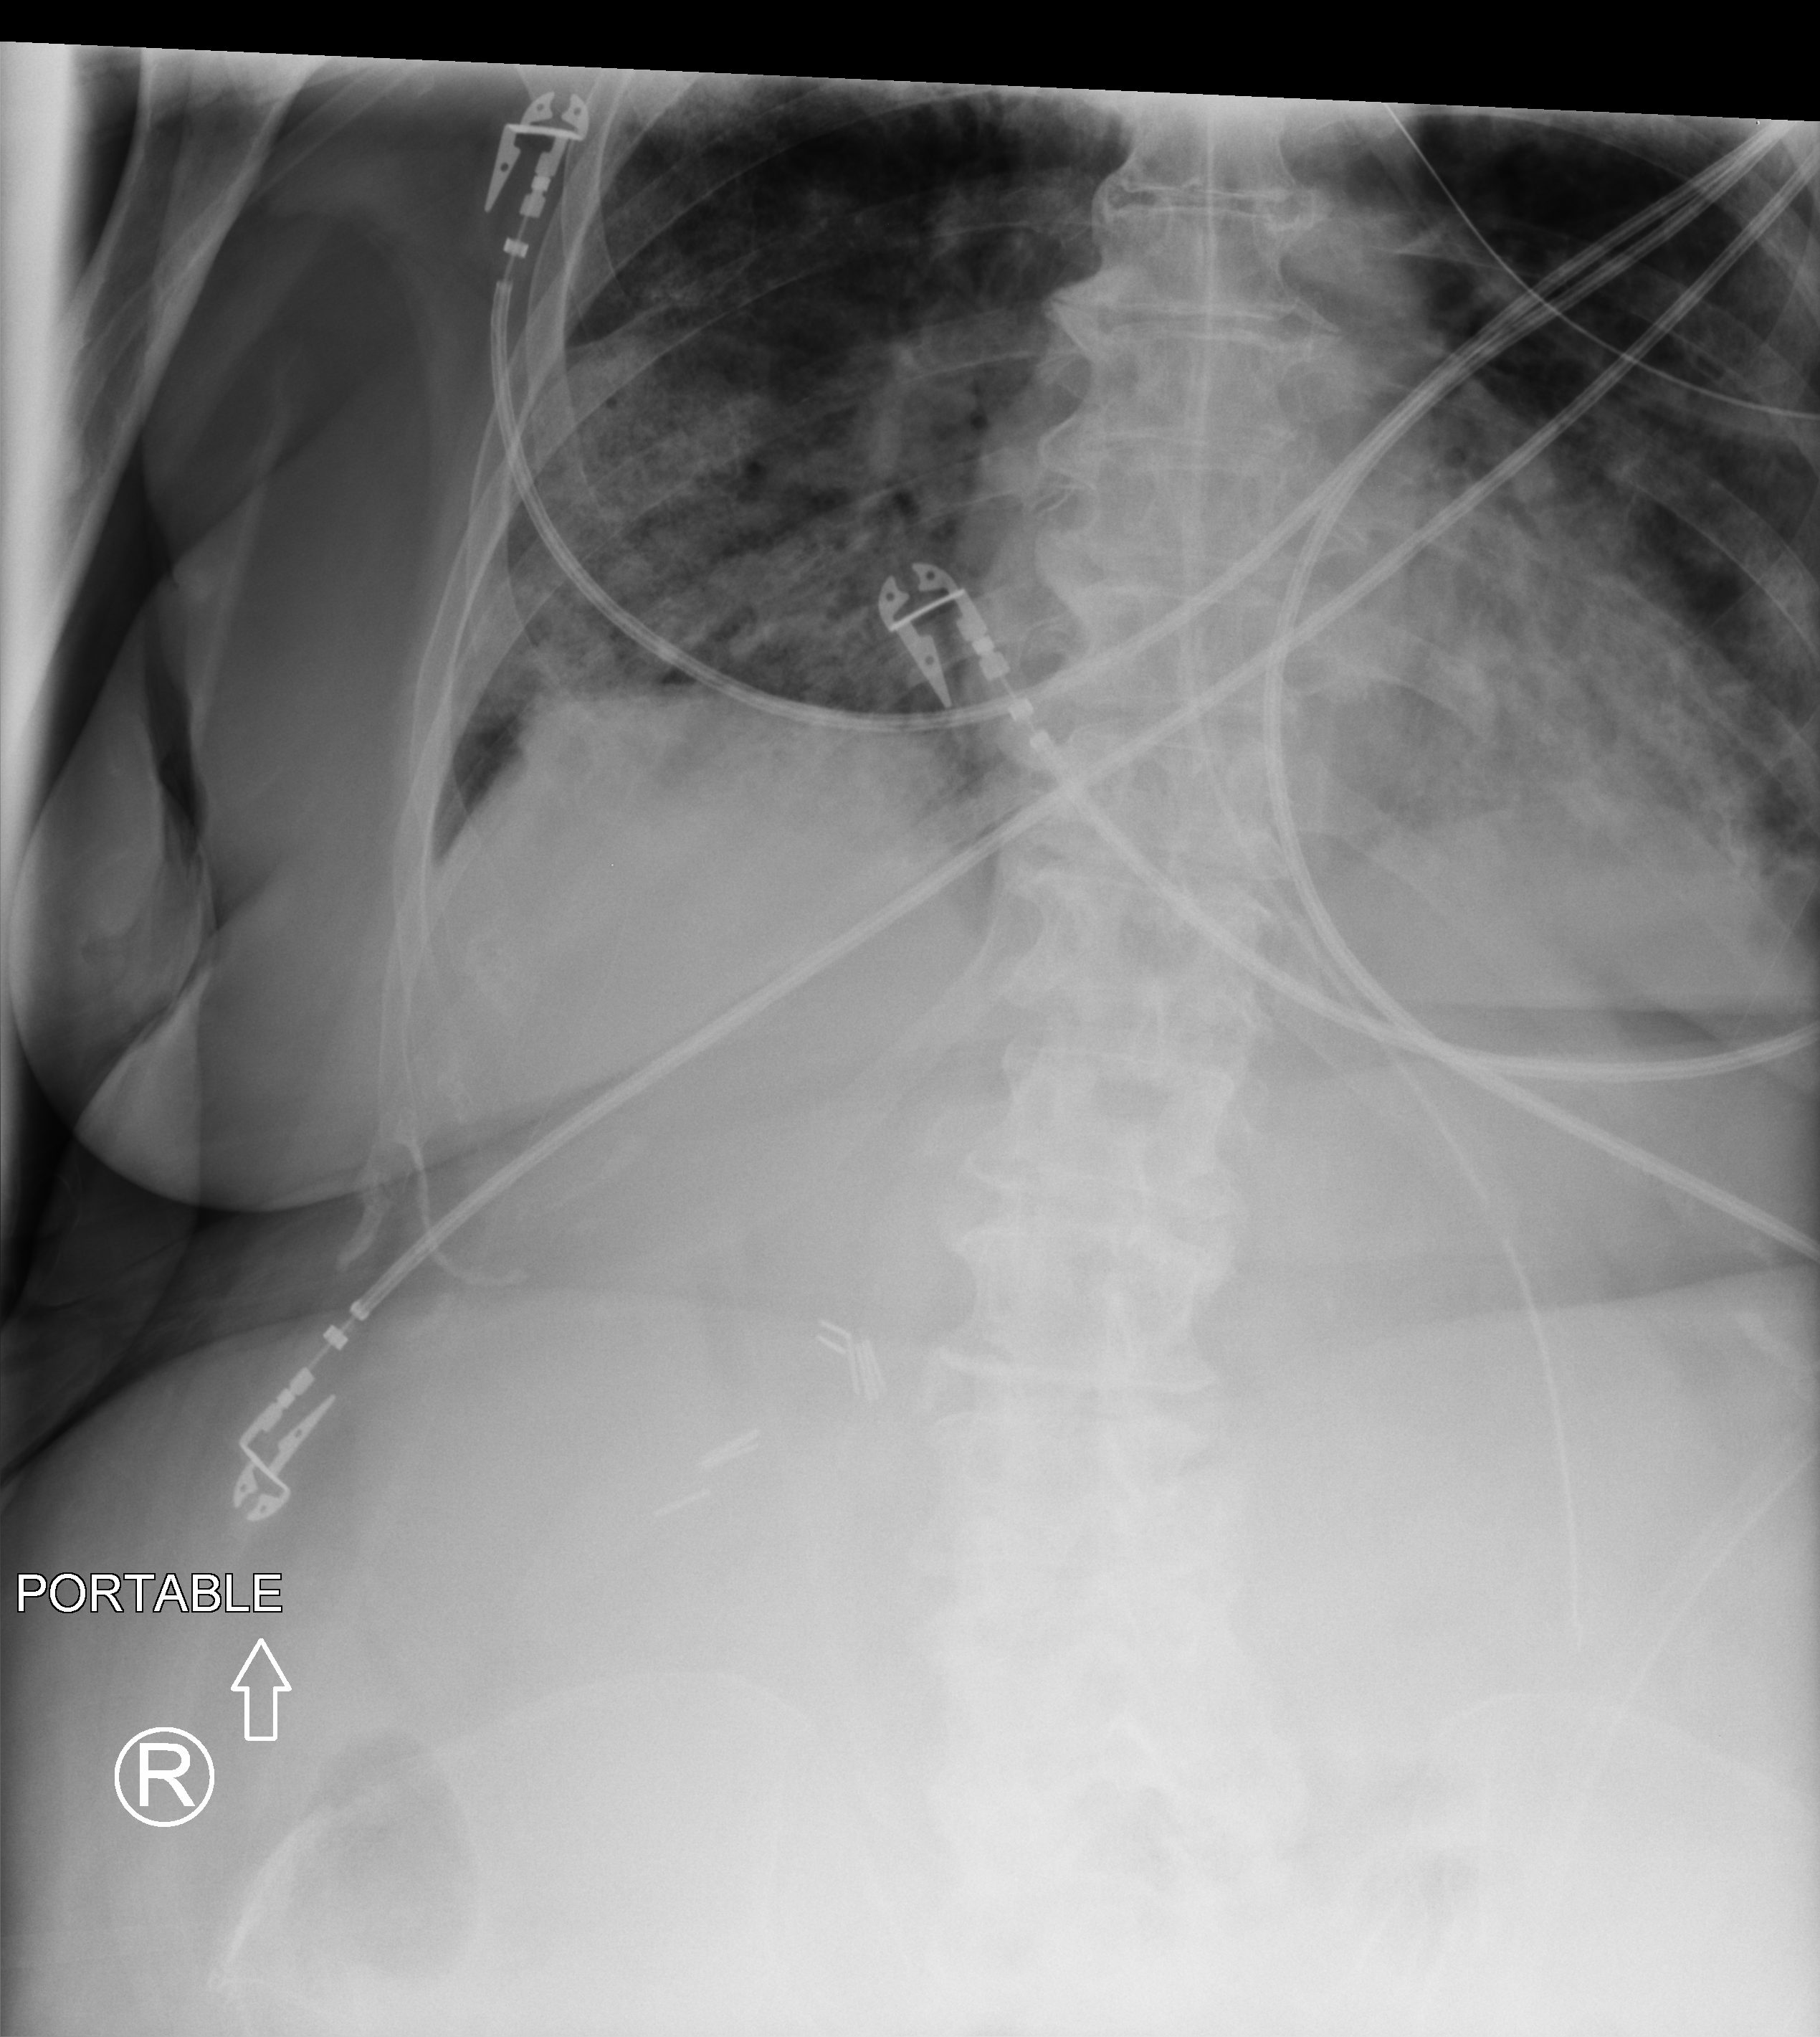
Bedside abdomen radiograph (computed radiography). Female patient hospitalised with COVID-19, age 75–90 years.
Hospital-stay facts (about this admission, not read from this image; timing relative to this image not recorded): mechanically ventilated during this hospital stay: yes; chronic kidney disease (admission record): no.